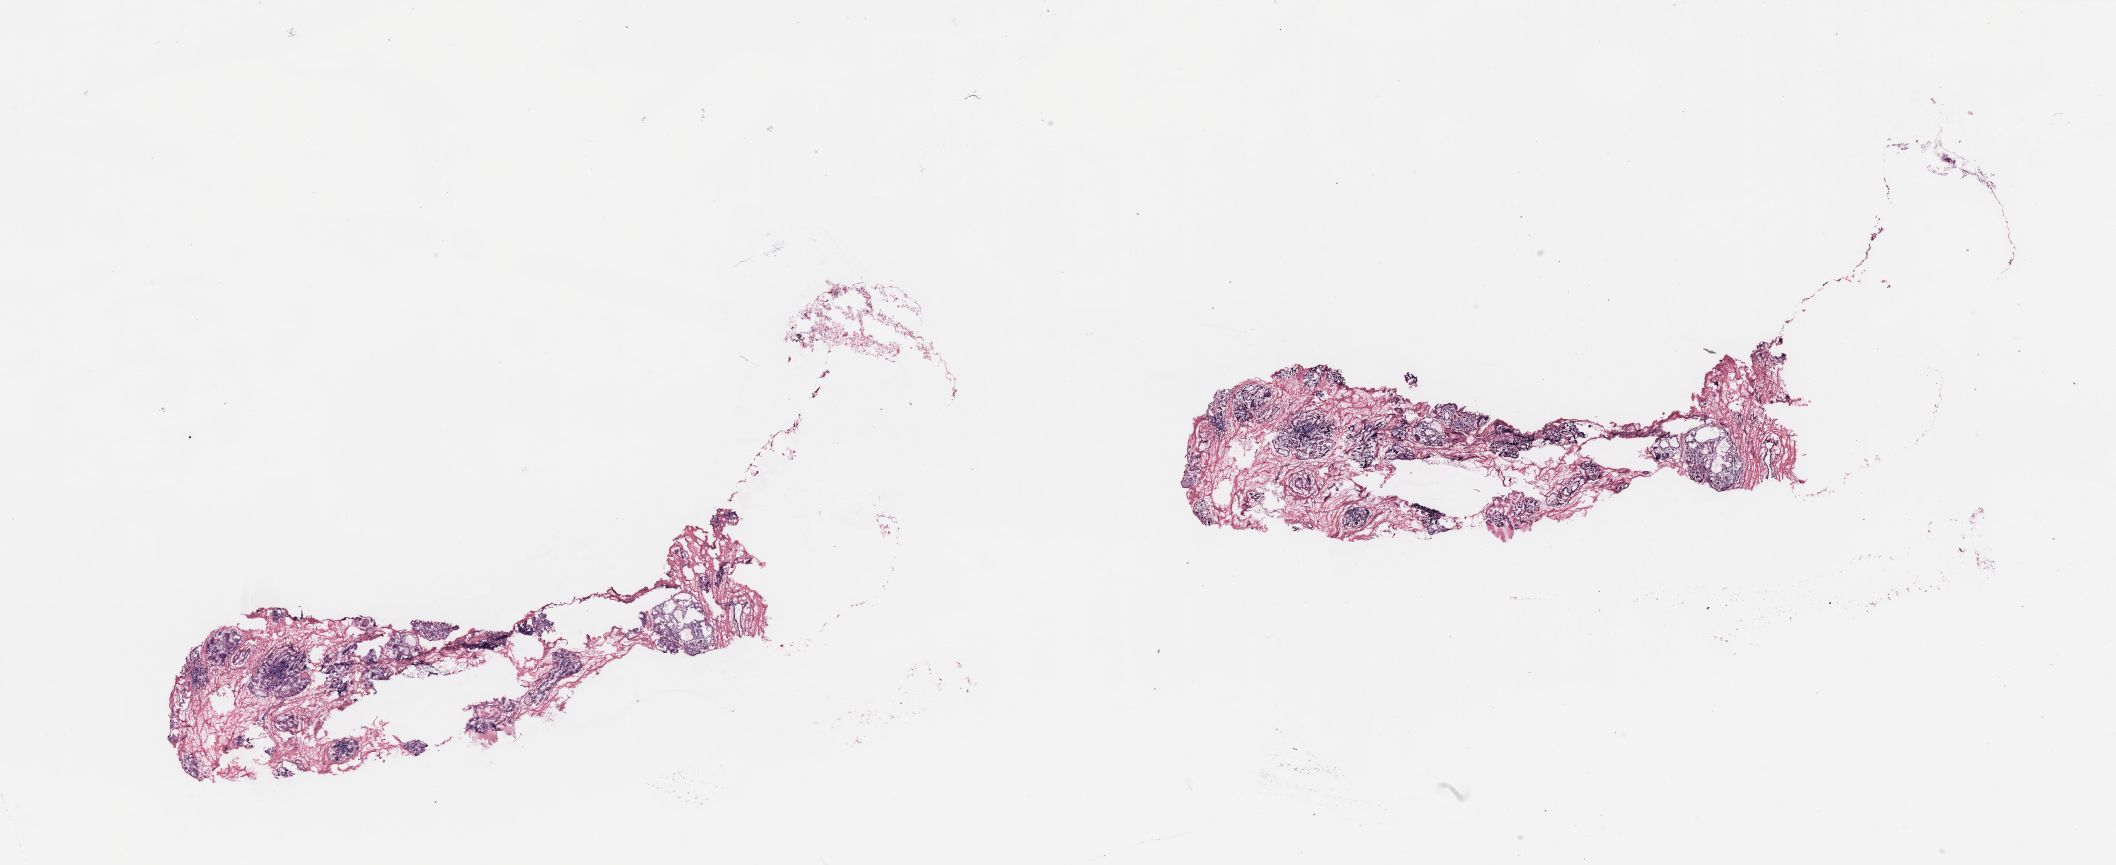
Digitized H&E tissue section (whole slide) — low-resolution overview of the scanned area, about 33.5 x 13.7 mm; breast, tissue type not recorded.
Patient diagnosis (cohort enrolment): breast cancer (breast).